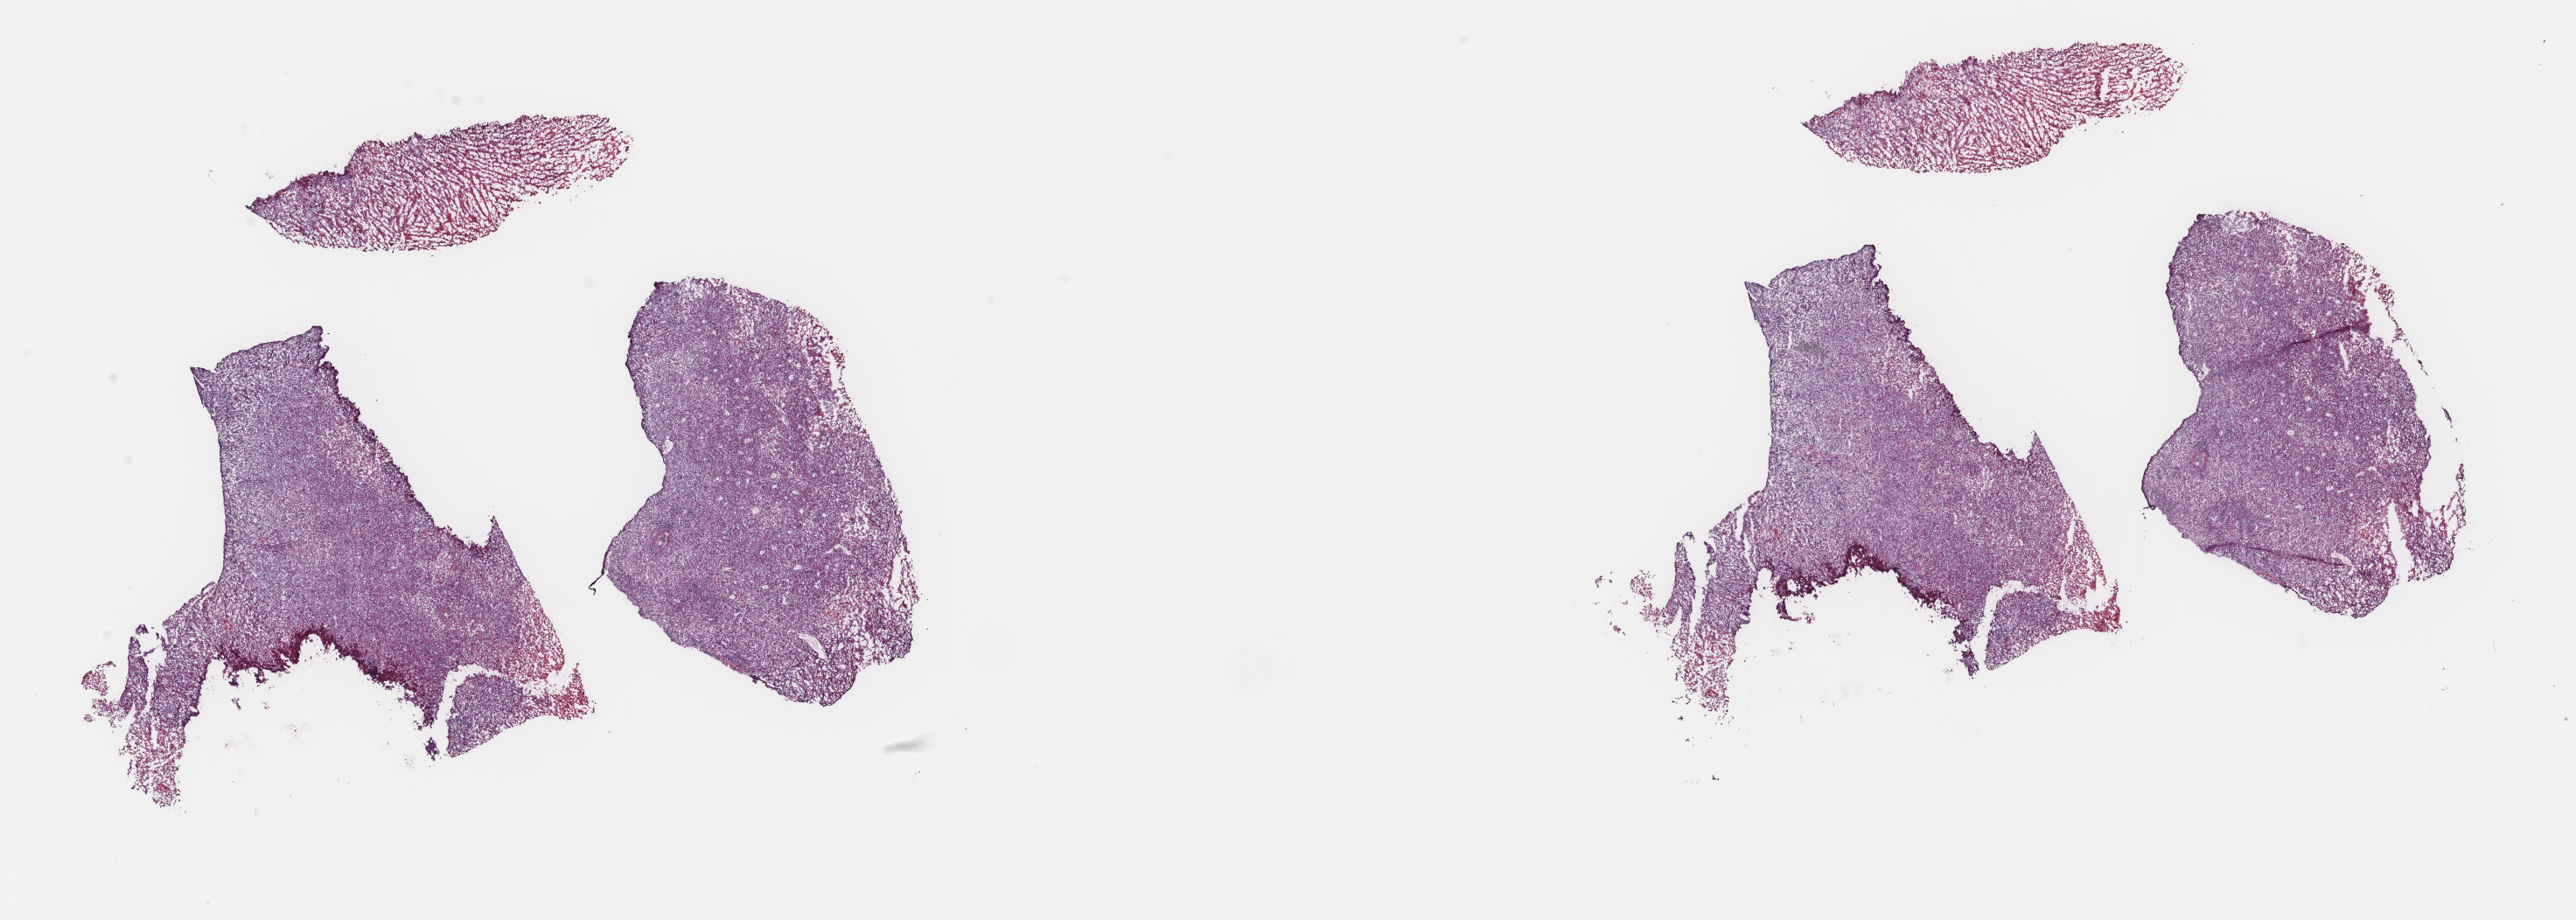
H&E whole-slide image — a low-resolution overview of the entire scanned area, about 23.4 x 8.3 mm, frozen section from the top of the tissue portion, bladder, primary tumour sample. Female patient. Histologic grade: high grade. Pathologist review of this section (percent, as recorded): tumour cells 70%, tumour nuclei 80%, normal cells 0%, stromal cells 10%, necrosis 20%. Infiltration values recorded for this section: lymphocyte infiltration 12%, monocyte infiltration 0%, neutrophil infiltration 1%.
- pathologic diagnosis: Transitional cell carcinoma
- lymph nodes positive (case pathology): 0 of 8 examined
- TNM: T2b N0 MX
- AJCC pathologic stage: II (7th edition)